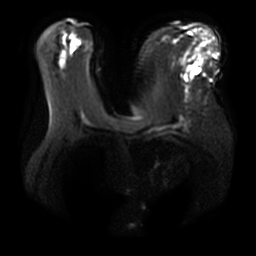
Breast MRI, one axial slice. Slice 19 of 36 in the series (ordered by position). Diffusion-weighted series; image 2 of 4 stored at this slice position (different b-values; order by instance number). 3 T. 5 mm slice thickness. 256 × 256 image matrix. Female patient.
Outlined on this slice (manually delineated by an expert):
- tumour on diffusion-weighted imaging: bounding box [x1, y1, x2, y2] px = [190, 63, 200, 74]